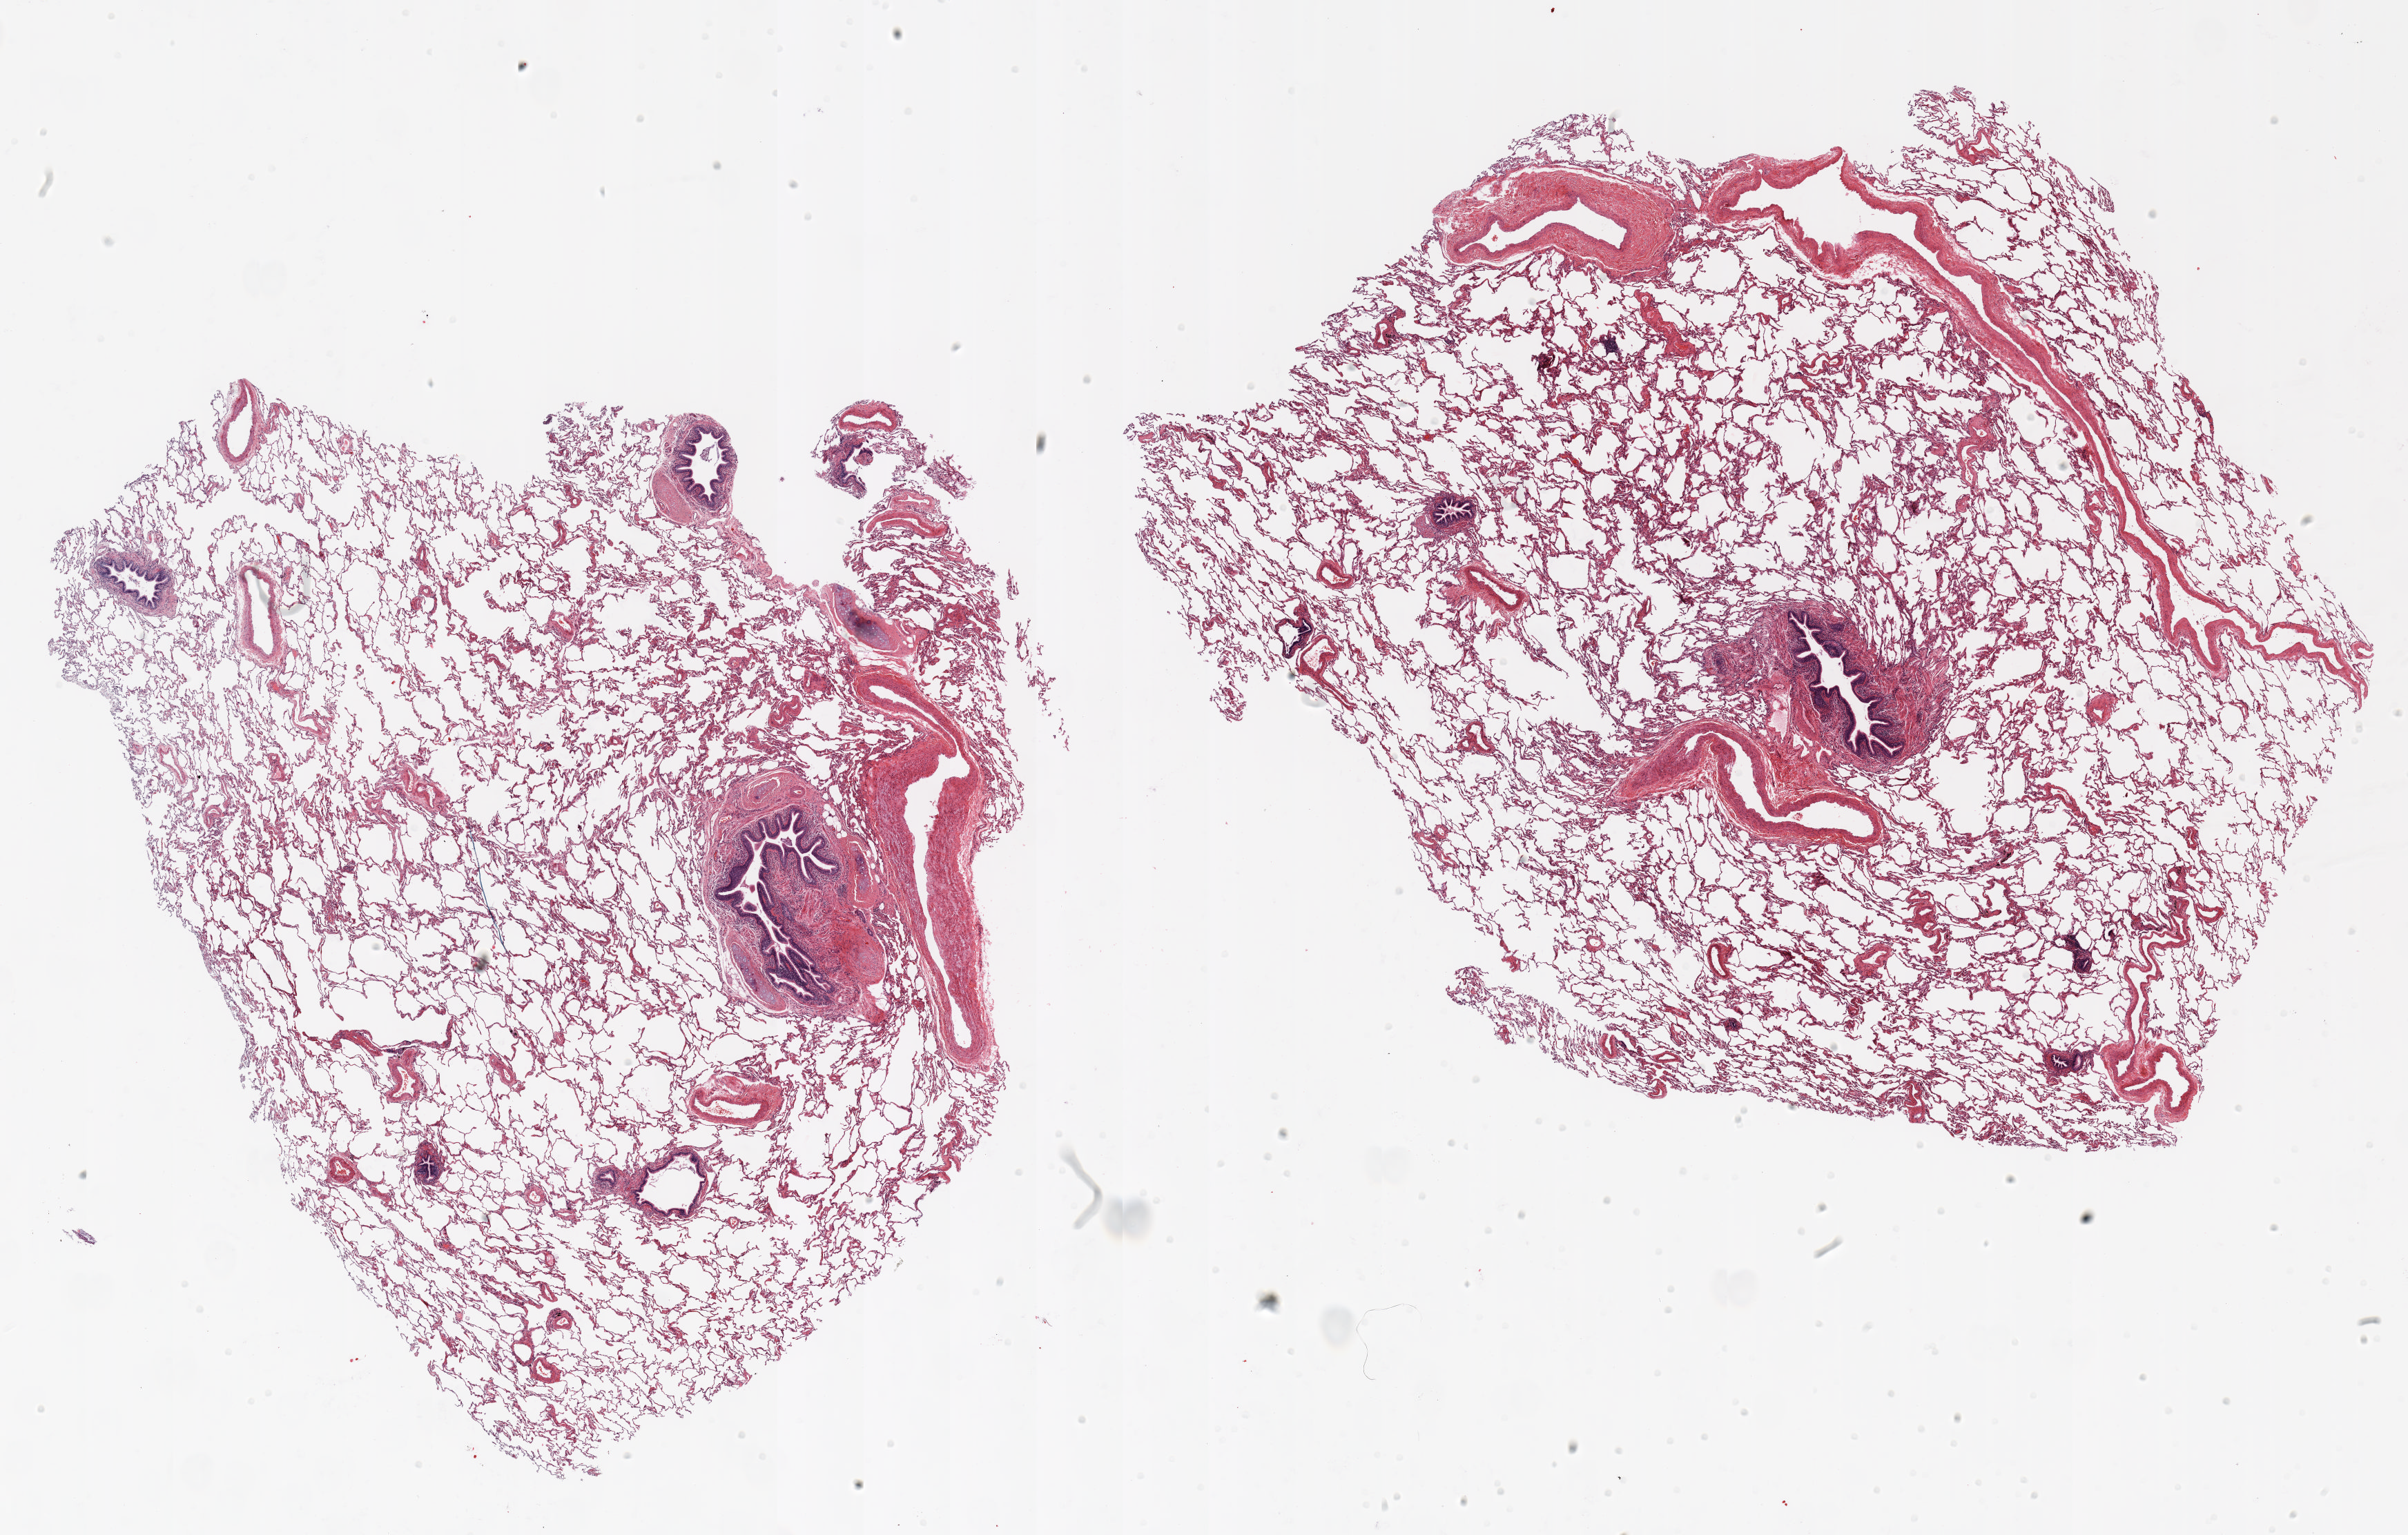
H&E whole-slide image — shown as a low-resolution overview of the whole scanned area (about 28.0 x 17.9 mm, acquisition: 20x scan). Formalin-fixed paraffin-embedded (FFPE) section. Lung. Female patient, aged 59 at enrolment. Grade: moderately differentiated (G2).
• stage (AJCC 6th edition): IA
• participant's lung-cancer diagnosis: Squamous cell carcinoma, NOS
• primary tumour location (clinical record): right lower lobe
• tumour size (pathology): 13 mm